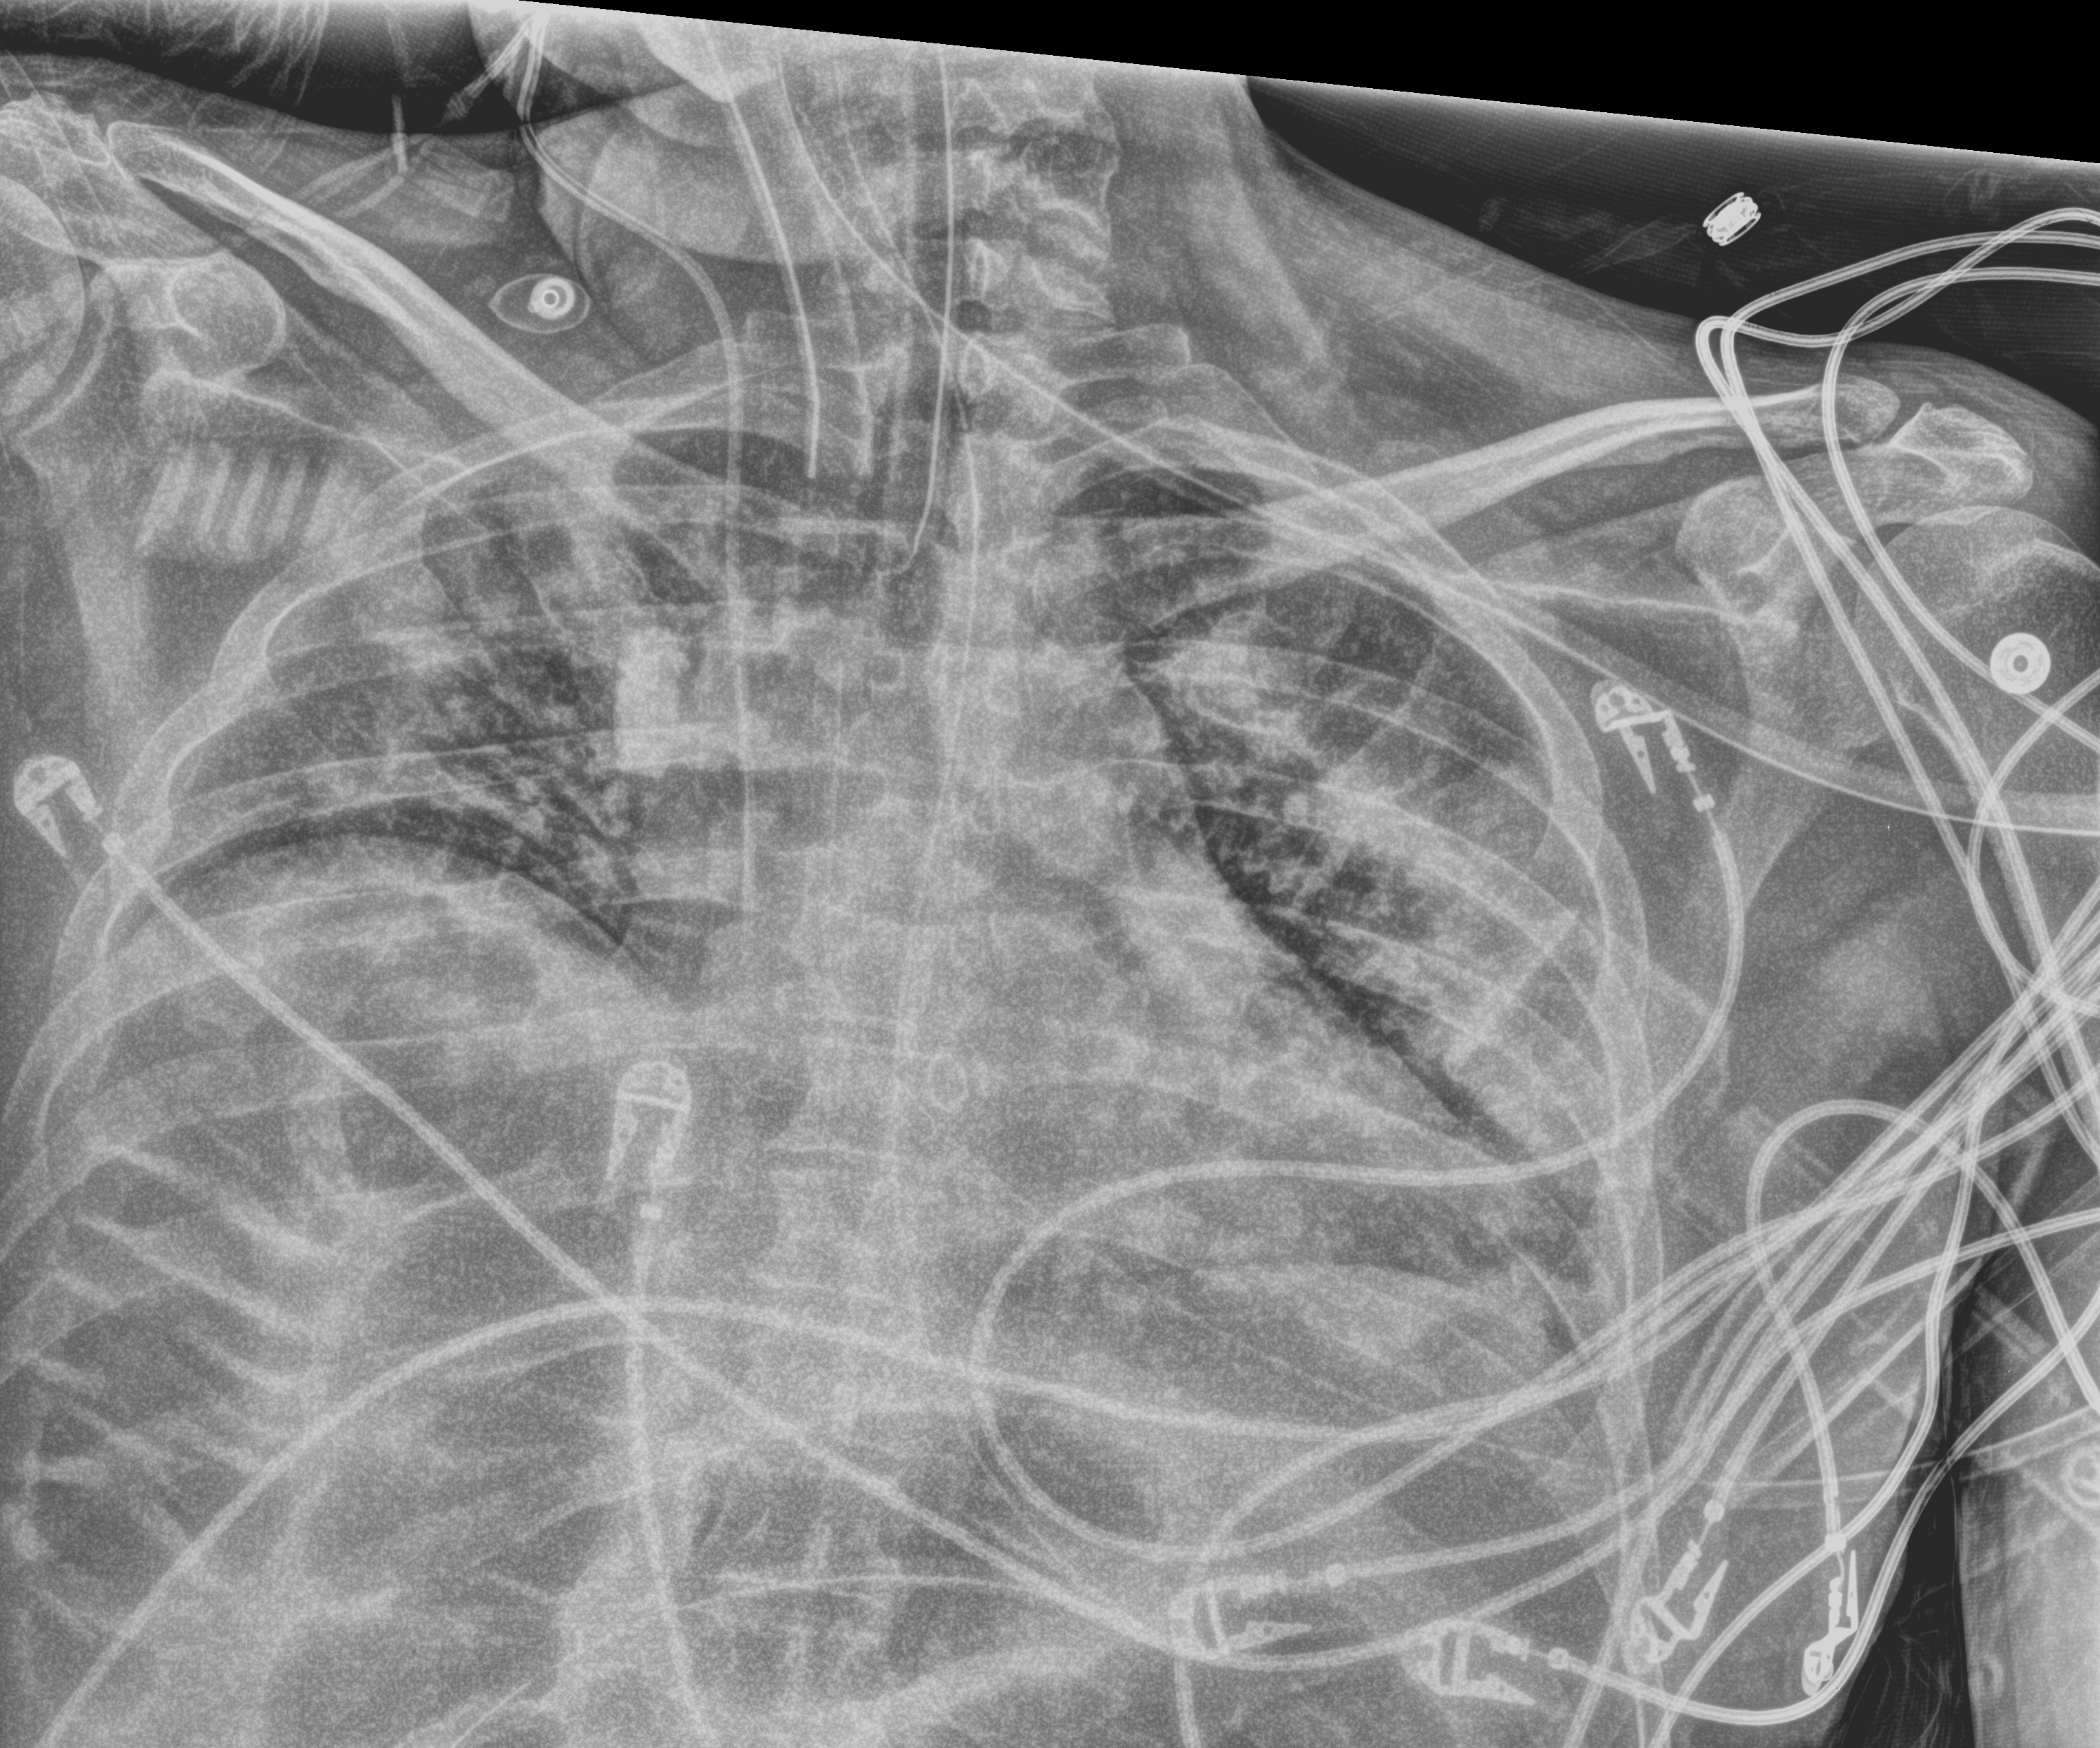
Chest X-ray (portable). Male patient hospitalised with COVID-19, age 18–59 years.
Hospital-stay facts (about this admission, not read from this image; timing relative to this image not recorded): COPD (admission record): no.